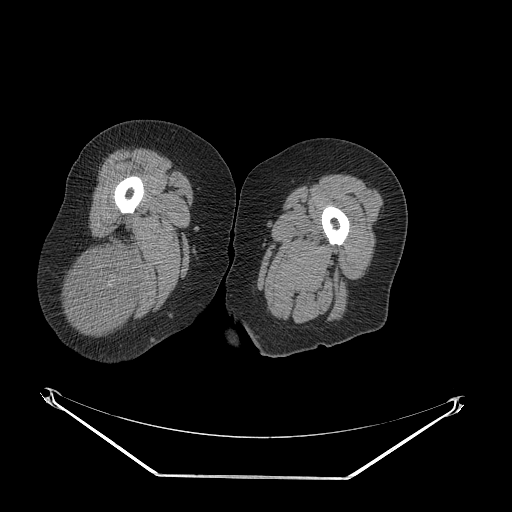
CT of an extremity soft-tissue mass (from a PET/CT study), one axial slice. Position 34 of 257 along the scan axis. Reconstruction kernel STANDARD. Soft-tissue window (W 400 / L 40 HU). 3.75 mm slice thickness. 512 × 512 image matrix, field of view 500 × 500 mm. Female patient. Case-level facts recorded for this patient, not image findings: histological type: synovial sarcoma; grade: intermediate; site of the primary tumour: right buttock.
Annotated regions visible in this slice (expert contour drawn on MRI and transferred to this co-registered scan by the dataset authors):
- gross tumour volume including surrounding oedema: bounding box [x1, y1, x2, y2] px = [66, 240, 138, 332]
- gross tumour volume (mass): [66, 247, 138, 332]